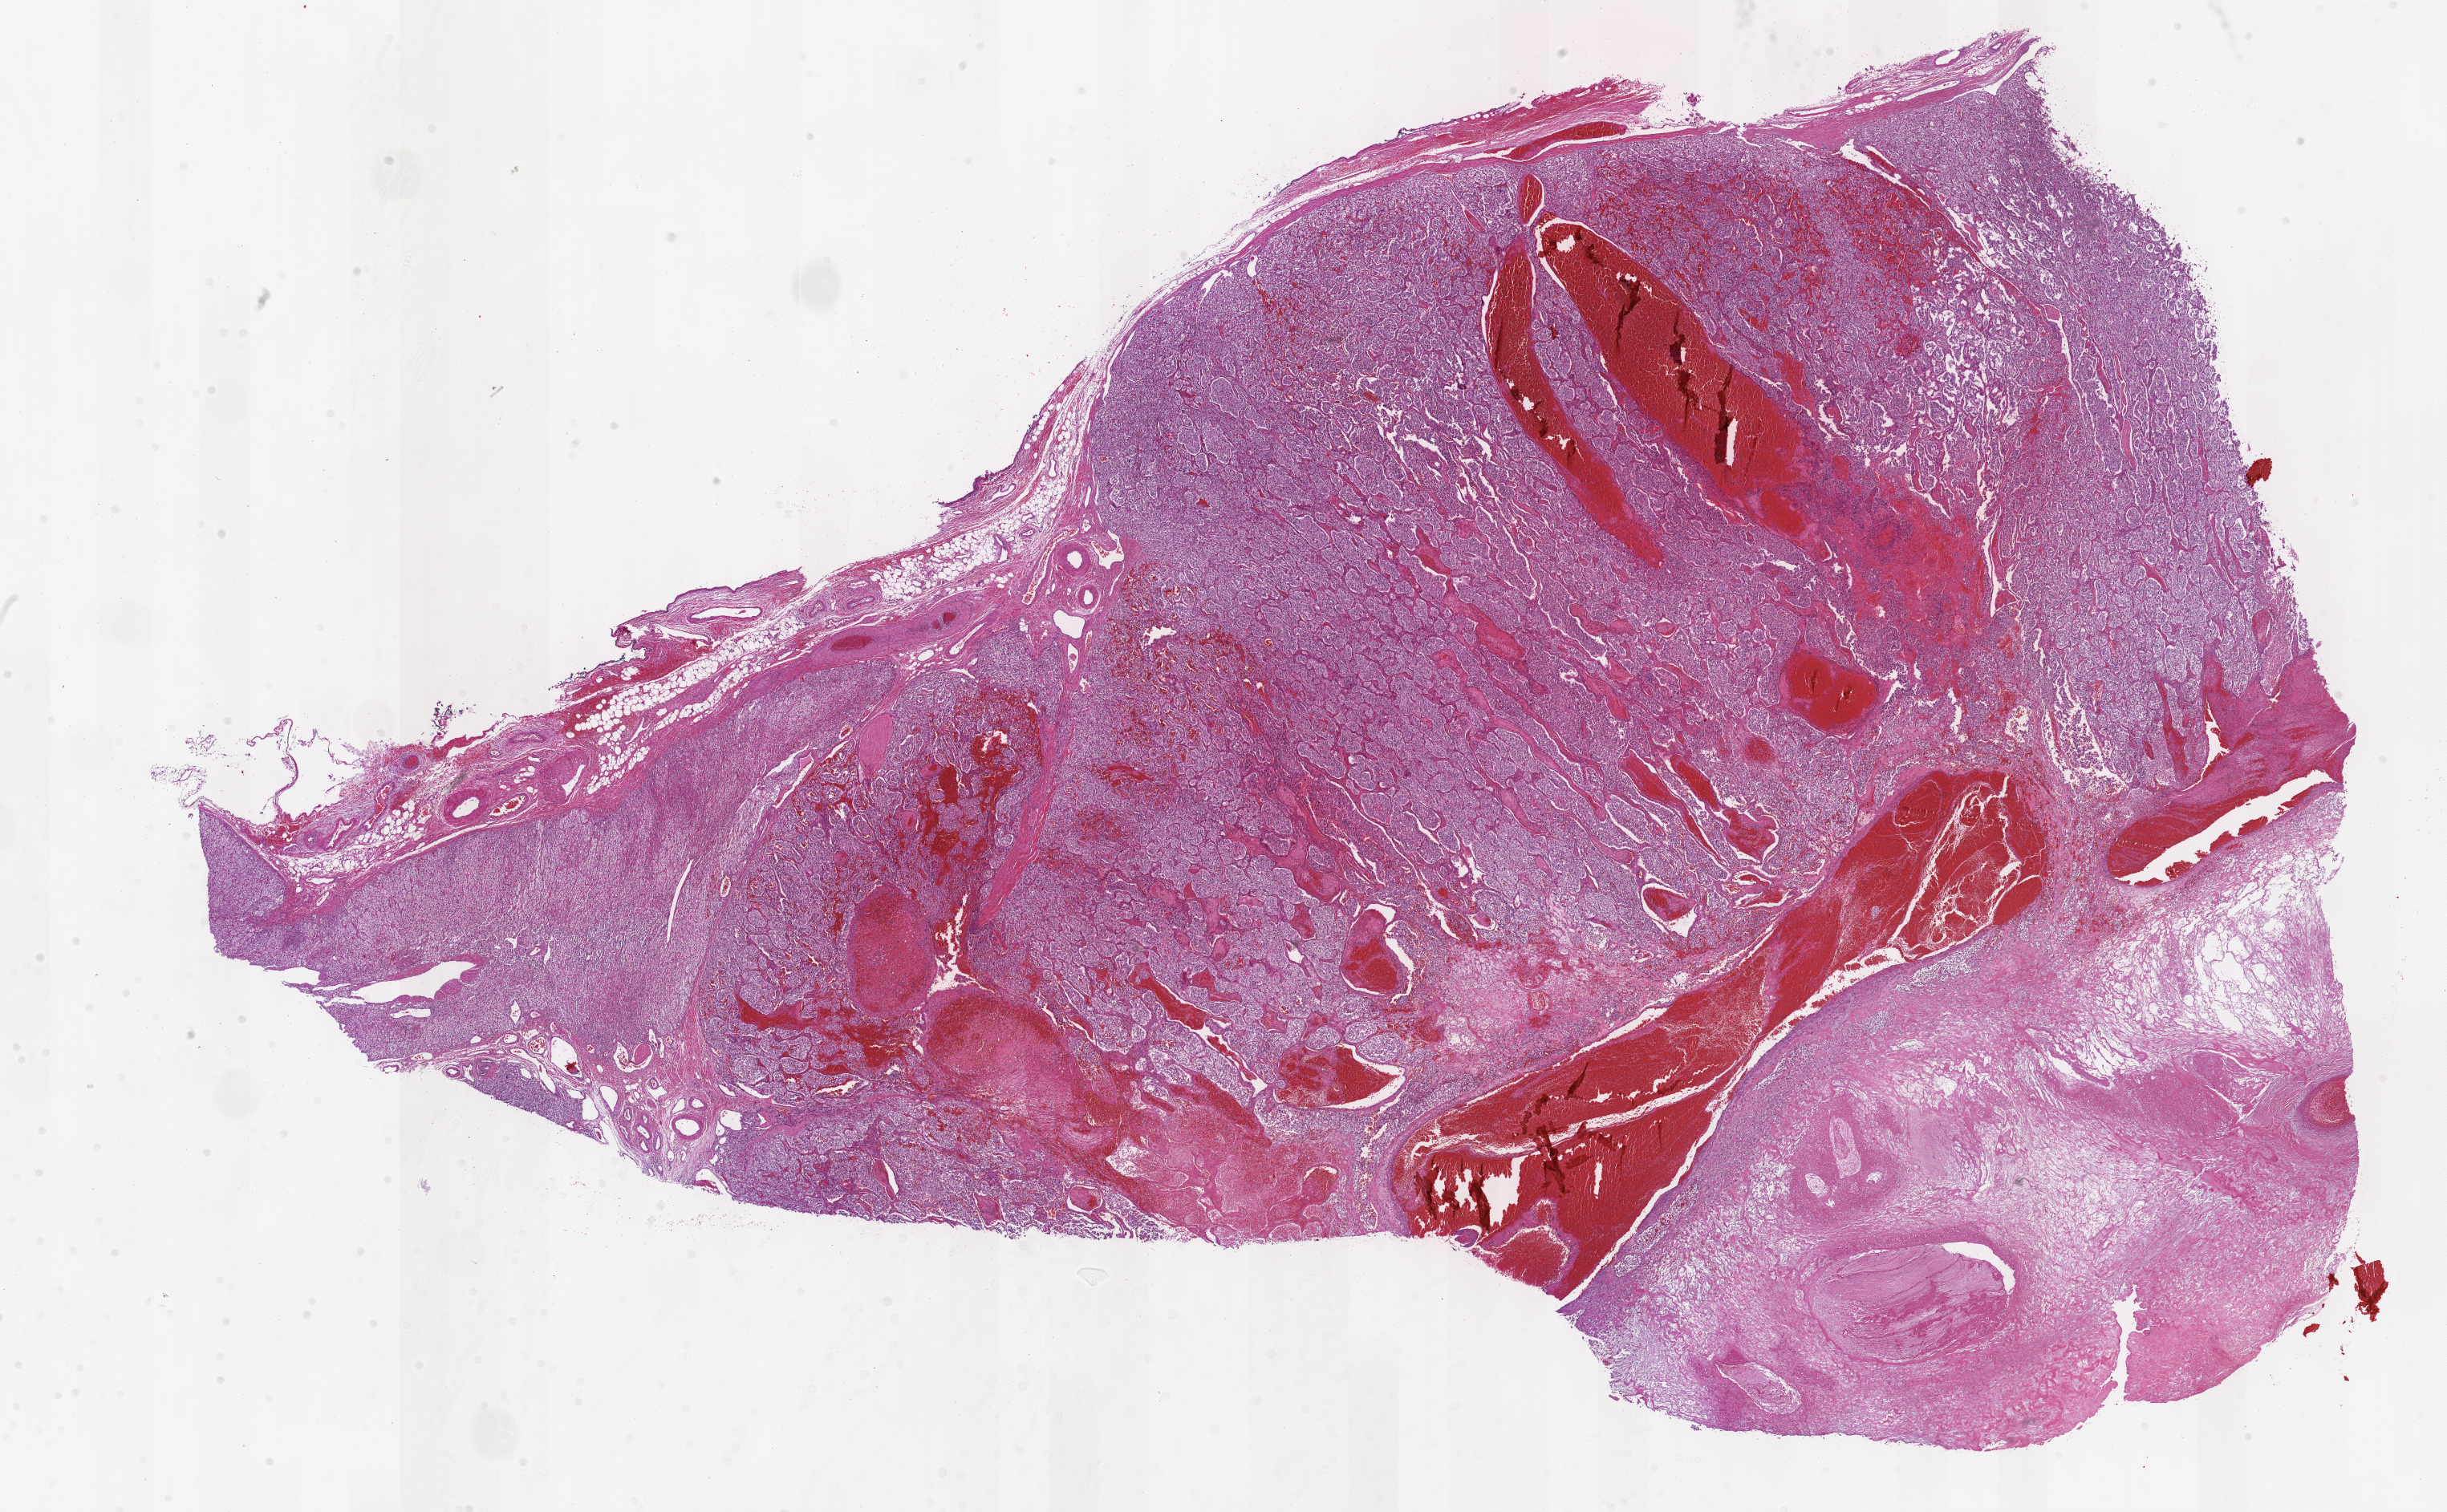
Whole-slide histology image, H&E — low-resolution overview of the scanned area, about 24.7 x 15.2 mm (acquisition: 40x scan); formalin-fixed paraffin-embedded (FFPE) diagnostic section; primary tumour sample from the retroperitoneum and peritoneum. Female patient; age at initial diagnosis 63 years.
* diagnosis: Pheochromocytoma, NOS (retroperitoneum)